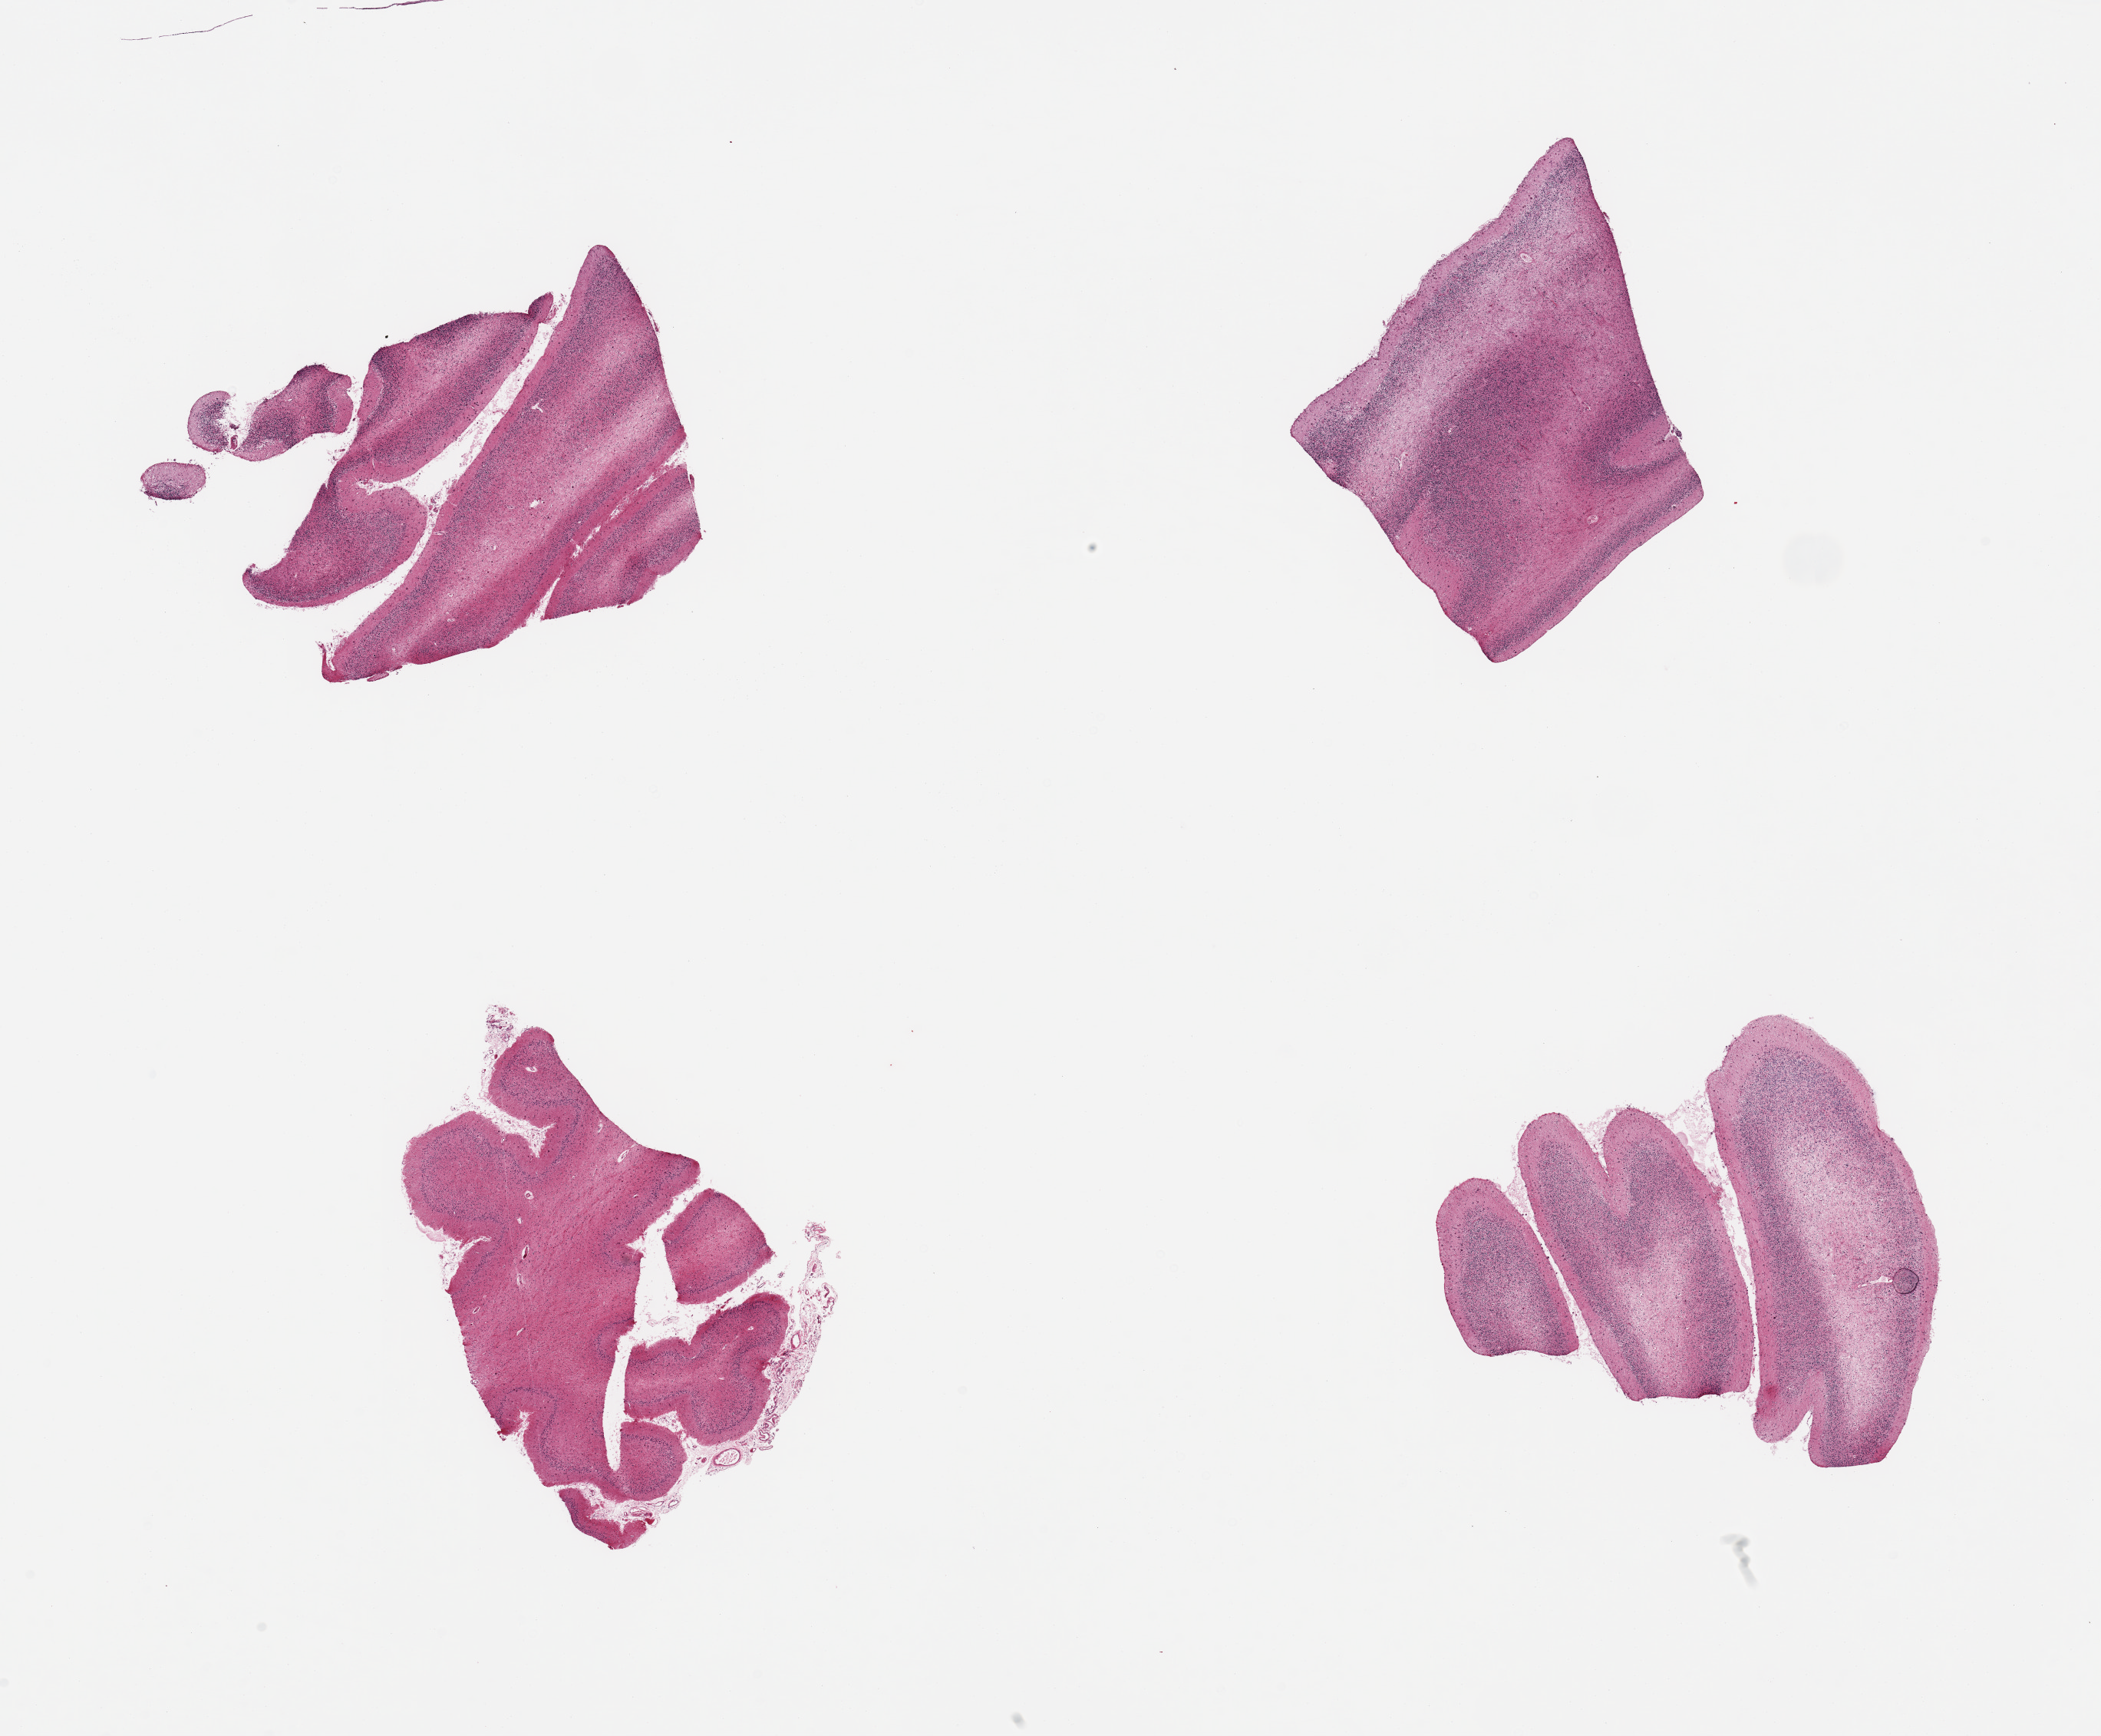
Digitized H&E-stained section, low-resolution overview of the scanned area, about 21.7 x 17.9 mm; PAXgene-fixed, paraffin-embedded tissue; target tissue: cerebellum; donor tissue sample. Donor sex: male.
Pathologist's review note for this sample: 4 pieces.